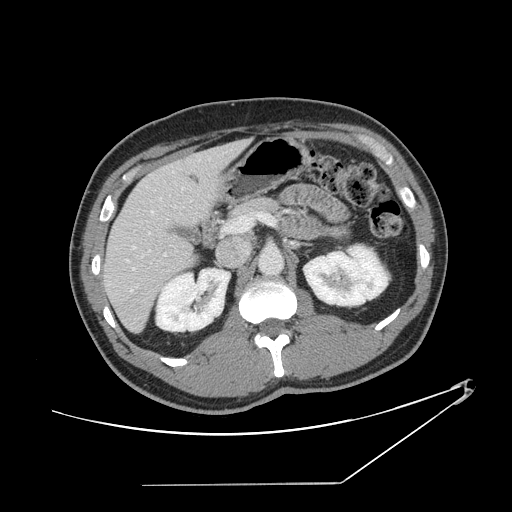
Contrast-enhanced abdominal CT, one axial slice; position 74 of 152 along the scan axis; 120 kVp; intravenous contrast given; soft-tissue window (W 400 / L 40 HU); 2.5 mm slice thickness; 512 × 512 image matrix, field of view 432 × 432 mm. Male patient, age 45 years. Case-level facts recorded for this patient, not image findings: diagnosis: colorectal cancer liver metastases, imaged before liver resection; multiple liver metastases: no; largest metastasis: 1 cm.
Annotated regions visible in this slice (expert manual segmentation):
- hepatic veins: bounding box (x1, y1, x2, y2) in pixels: (131, 160, 200, 292)
- liver: (105, 141, 248, 332)
- planned liver remnant (the part of the liver to remain after resection): (105, 159, 209, 332)
- portal vein (with intrahepatic branches): (127, 213, 274, 270)